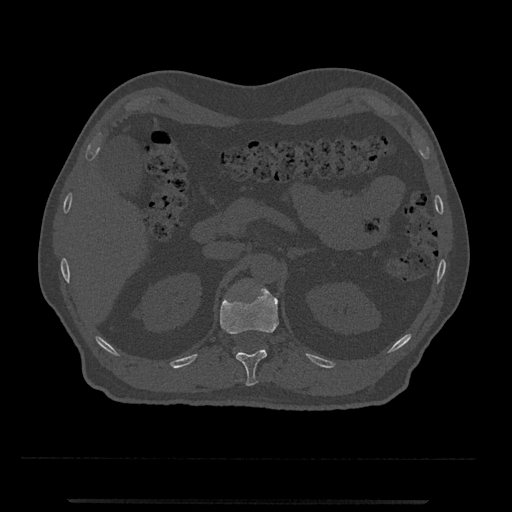
CT including the spine, one axial slice. Slice 383 of 797 in the series (ordered by position). Reconstruction kernel Br40s/3. 120 kVp. Bone window (W 1800 / L 400 HU). 0.5 mm slice thickness. 512 × 512 image matrix, field of view 419 × 419 mm. Male patient, age 63 years. From the clinical record (not read from this slice): primary cancer: prostate.
Structures marked on this image (semi-automatic segmentation, software-assisted and operator-edited):
- T12 vertebra: bounding box (x1, y1, x2, y2) in pixels: (220, 287, 279, 386)